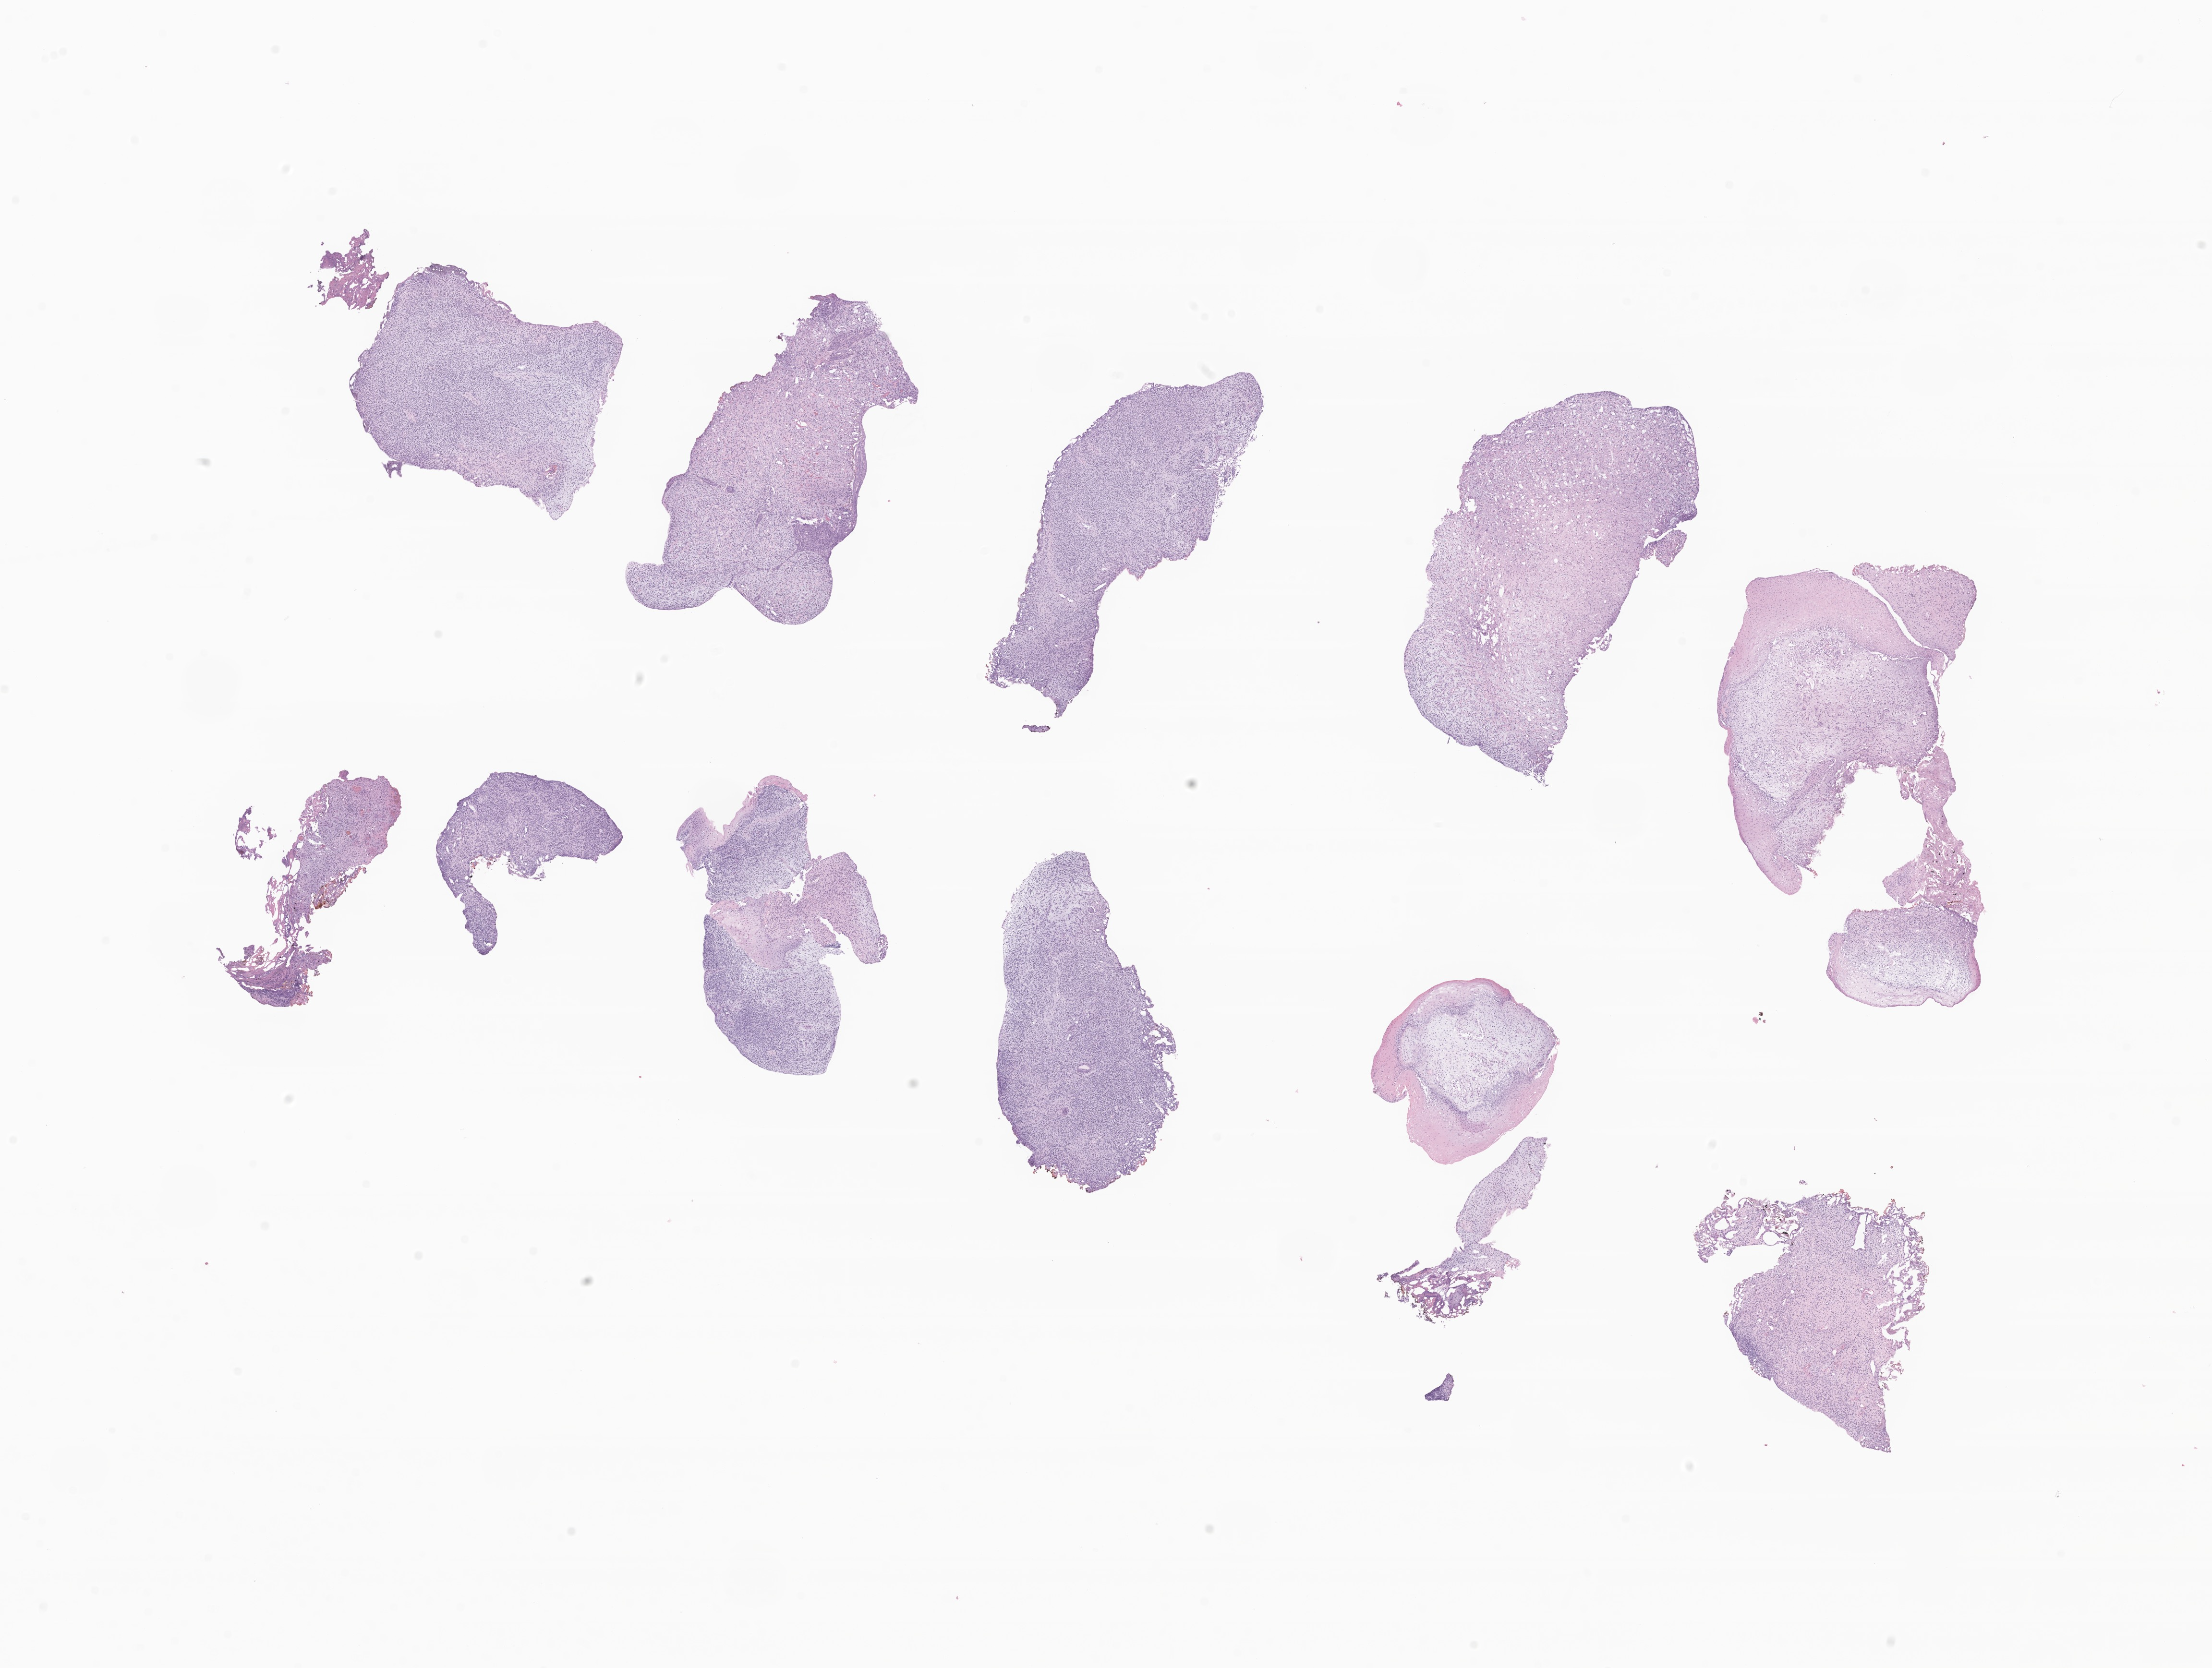
Digitized H&E-stained section of tumor tissue from the neck of urinary bladder, low-resolution overview of the scanned area, about 19.4 x 14.7 mm. Formalin-fixed paraffin-embedded section. Patient: male, age 42 months.
• diagnosis (ICD-O-3 morphology term): Embryonal rhabdomyosarcoma, NOS